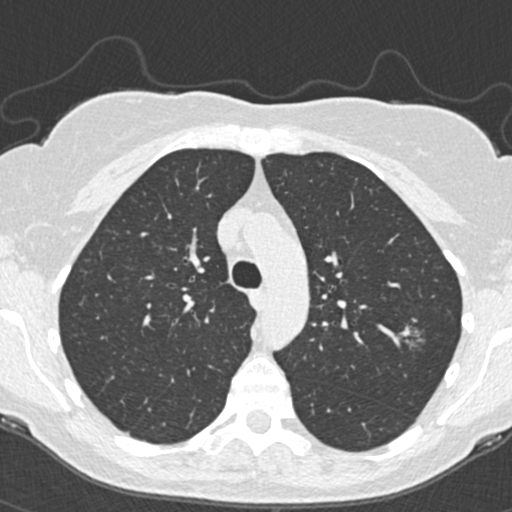
Low-dose screening chest CT, one axial slice; position 261 of 350 along the scan axis; reconstruction kernel B30f; 120 kVp; lung window (W 1500 / L -600 HU); 1 mm slice thickness; 512 × 512 image matrix, field of view 298 × 298 mm.
Structures marked on this image (manually delineated by an expert):
- lesion 1 (tumor, upper lobe of left lung): bounding box <400,326,425,348> (left, top, right, bottom; pixels)